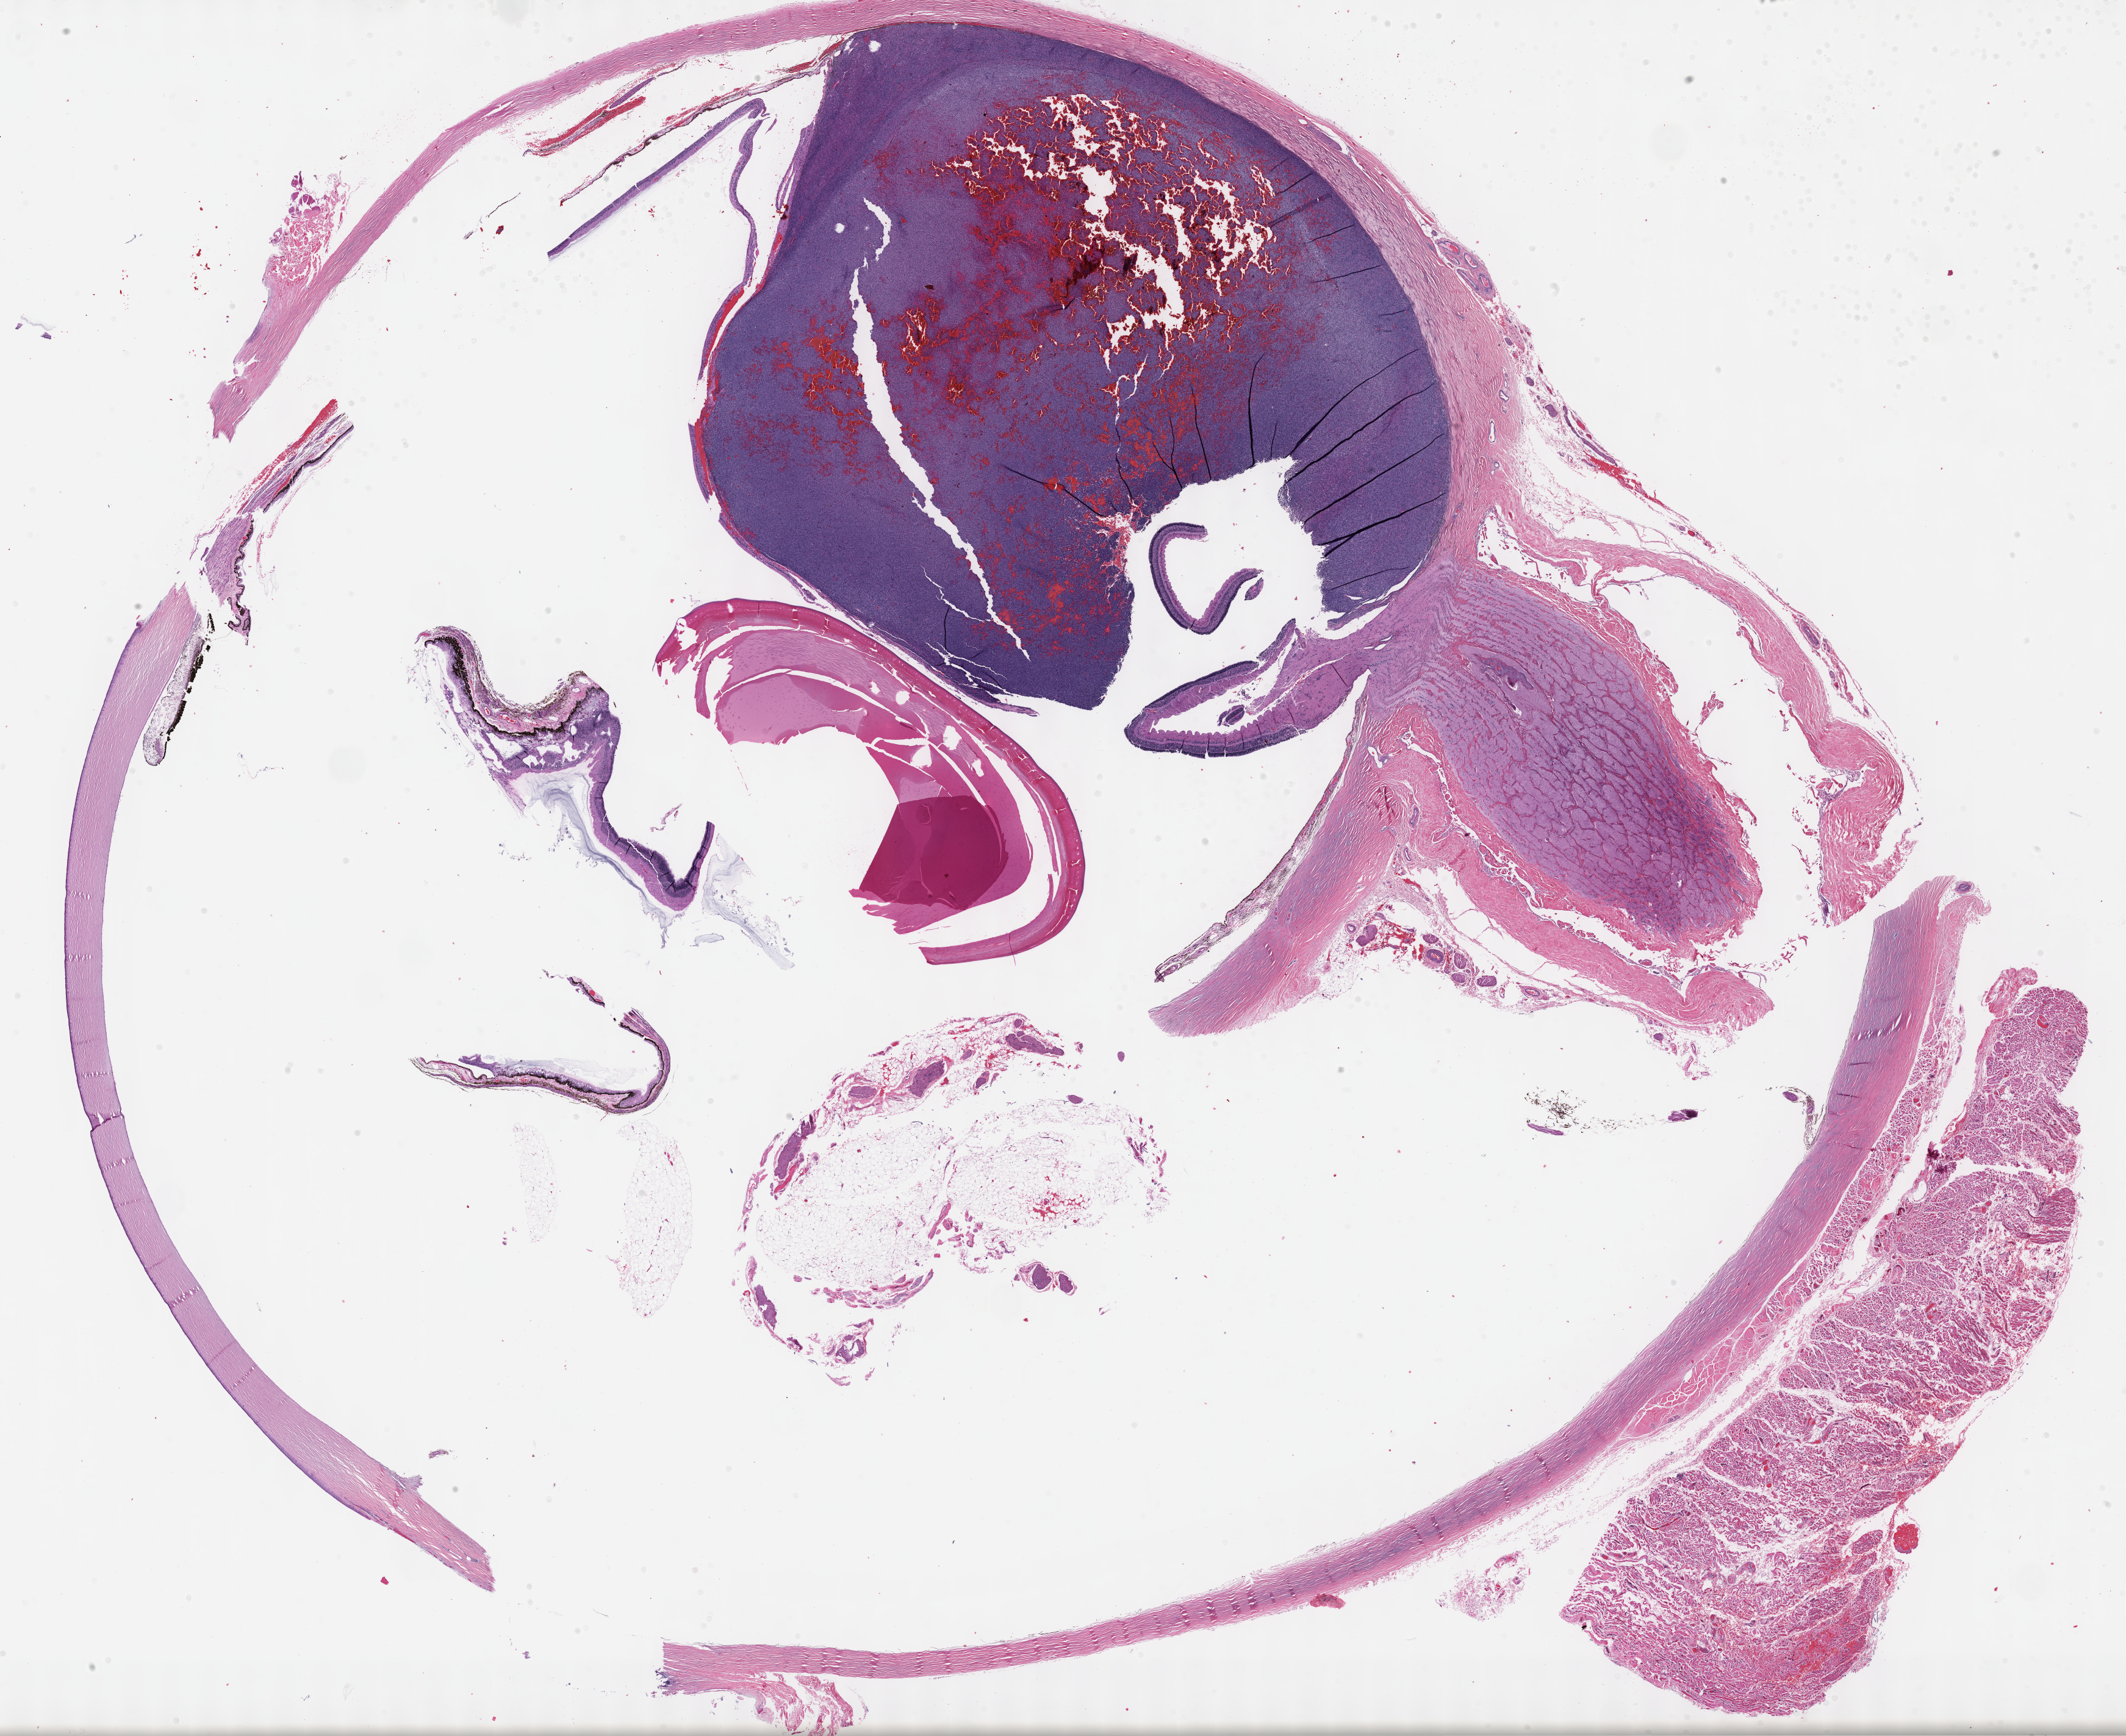
Digitized H&E tissue section (whole slide) — low-resolution overview of the scanned area, about 28.2 x 23.0 mm (slide scanned at 40x), FFPE section, sample: primary tumour, uvea. Male patient; age at initial diagnosis 63 years.
TNM: T4a N0 M0. Diagnosis: Mixed epithelioid and spindle cell melanoma. AJCC pathologic stage: IIIA (7th edition).